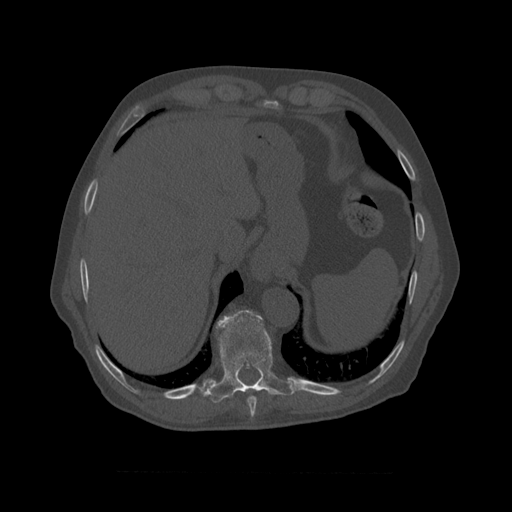
CT including the spine, one axial slice. Reconstruction kernel STANDARD. 120 kVp. Bone window (W 1800 / L 400 HU). 1.25 mm slice thickness. 512 × 512 image matrix, field of view 405 × 405 mm. Patient age 75 years. From the clinical record (not read from this slice): primary cancer: prostate.
Annotated regions visible in this slice (semi-automatically segmented with operator editing):
- T8 vertebra: bounding box (x1, y1, x2, y2) in pixels: (247, 396, 257, 410)
- T9 vertebra: (213, 310, 295, 398)